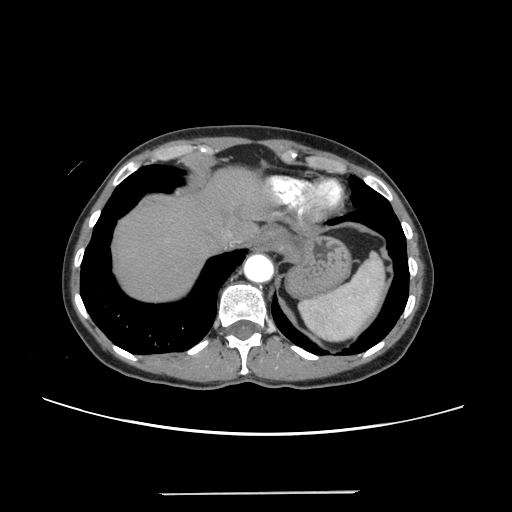
Contrast-enhanced abdominal CT, one axial slice. Position 211 of 240 along the scan axis. 120 kVp. Intravenous contrast given. Soft-tissue window (W 400 / L 40 HU). 1.25 mm slice thickness. 512 × 512 image matrix. Female patient, age 60 years. From the clinical record (not read from this slice): diagnosis: colorectal cancer liver metastases, imaged before liver resection.
Structures marked on this image (expert manual segmentation):
- hepatic veins: bounding box <222,230,233,241> (left, top, right, bottom; pixels)
- liver: <113,169,266,302>
- planned liver remnant (the part of the liver to remain after resection): <113,169,266,302>